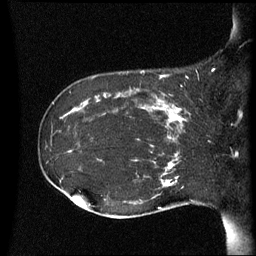
Breast MRI (dynamic contrast-enhanced), one sagittal slice; position 21 of 60 along the scan axis; dynamic contrast-enhanced series, image 2 of 3 at this slice position (ordered by acquisition); 1.5 T; TE 4.2 ms, TR 8.4 ms; 256 × 256 image matrix, field of view 220 × 220 mm. Female patient, age 41 years. Case-level facts recorded for this patient, not image findings: setting: breast cancer imaged before/during neoadjuvant chemotherapy; receptor status: HER2-positive.
Outlined on this slice (semi-automatic segmentation, software-assisted and operator-edited):
- analysis volume of interest (the breast-tissue region the enhancement analysis was run in; not a lesion): bounding box (x1, y1, x2, y2) in pixels: (122, 84, 195, 137)
- tumour enhancement mask (voxels above the 70 % enhancement threshold inside the analysis volume of interest): (137, 92, 187, 137)